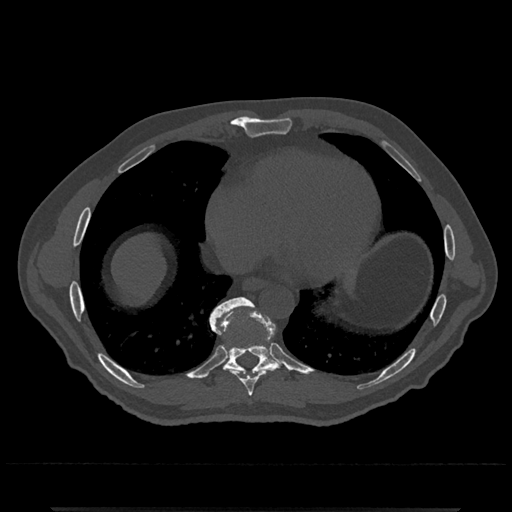
CT including the spine, one axial slice; position 640 of 797 along the scan axis; reconstruction kernel Br40s/3; 120 kVp; bone window (W 1800 / L 400 HU); 512 × 512 image matrix, field of view 393 × 393 mm. Male patient, age 67 years. Case-level facts recorded for this patient, not image findings: primary cancer: prostate.
Annotated regions visible in this slice (semi-automatically segmented with operator editing):
- T8 vertebra: bounding box (x1, y1, x2, y2) in pixels: (214, 331, 263, 396)
- T9 vertebra: (209, 297, 281, 375)